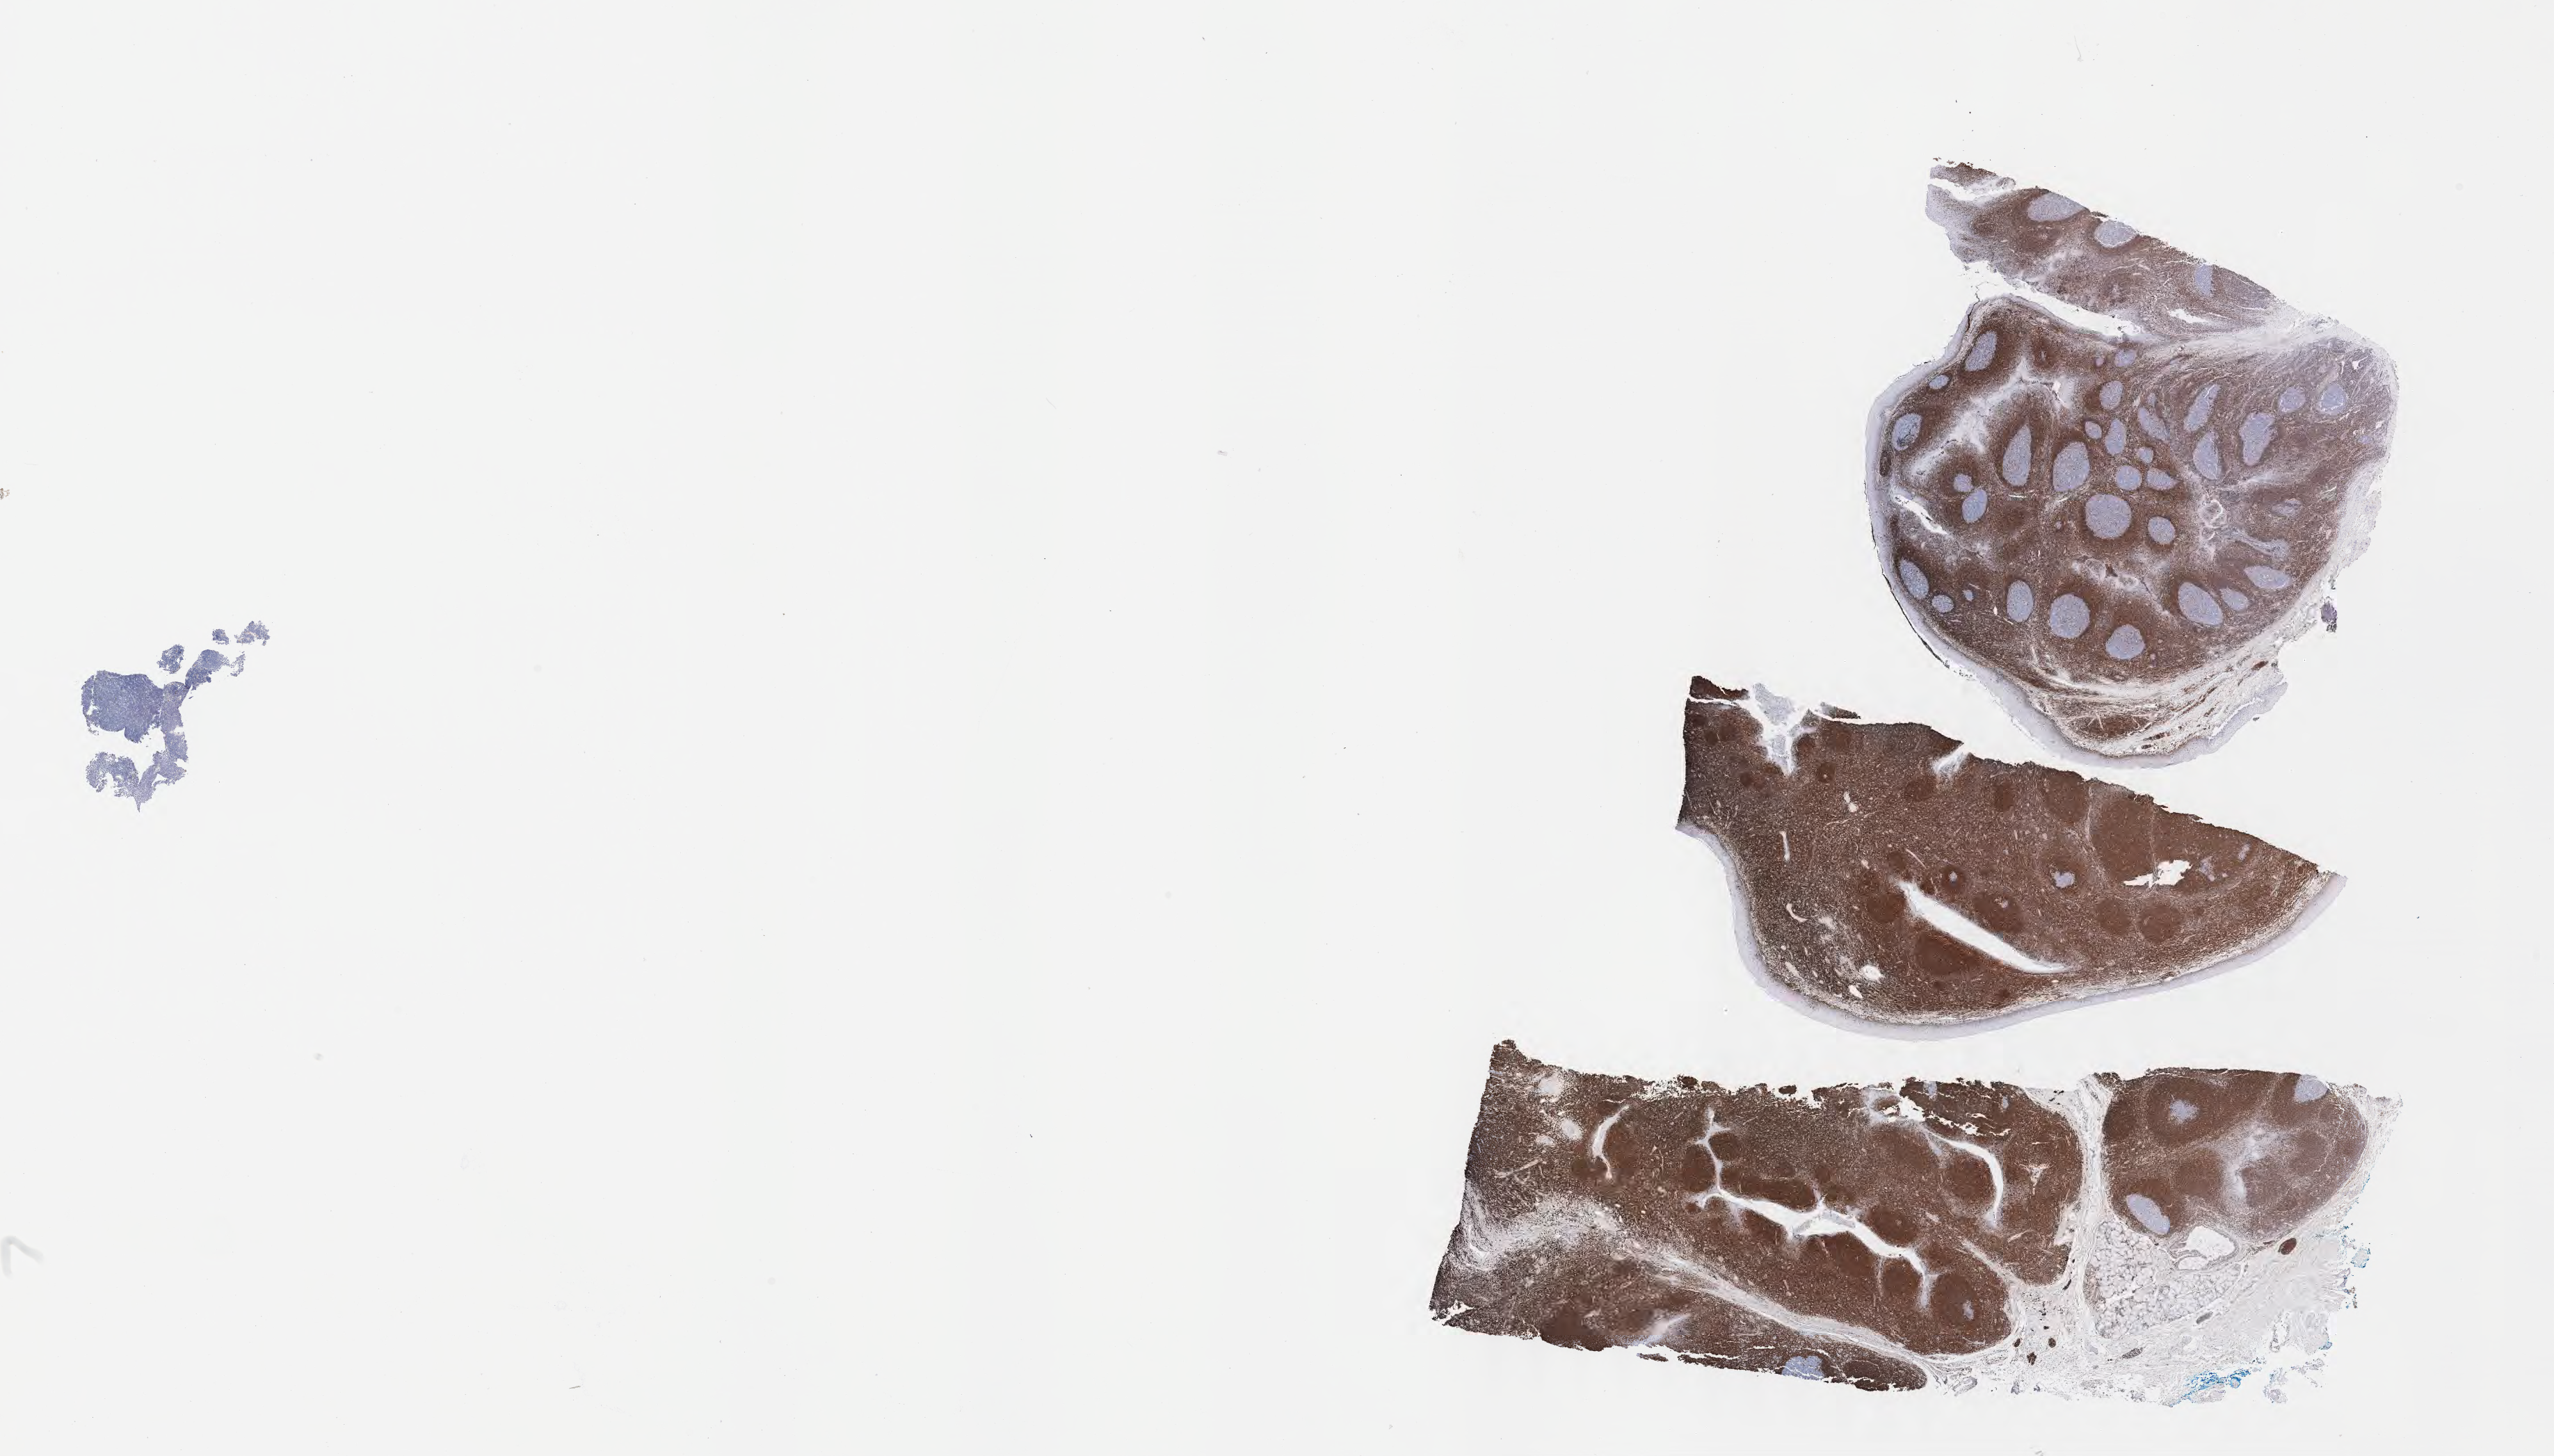
IHC for BCL2, whole-slide image — whole scanned area (about 29.7 x 16.9 mm) shown as a low-resolution overview. Tumor tissue. Male, age 8 years at initial diagnosis.
Diagnosis: Burkitt lymphoma, NOS.